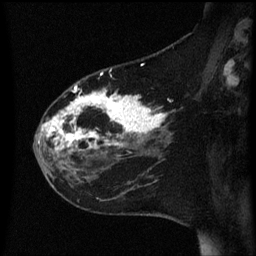
Breast MRI (dynamic contrast-enhanced), one sagittal slice. Position 20 of 60 along the scan axis. Dynamic contrast-enhanced series, image 2 of 3 at this slice position (ordered by acquisition). 1.5 T. TE 4.2 ms, TR 8.4 ms. 2.2 mm slice thickness. 256 × 256 image matrix, field of view 200 × 200 mm. Patient: female, 35 years. Case-level facts recorded for this patient, not image findings: setting: breast cancer imaged before/during neoadjuvant chemotherapy; receptor status: HER2-positive.
Structures marked on this image (semi-automatic segmentation, software-assisted and operator-edited):
- analysis volume of interest (the breast-tissue region the enhancement analysis was run in; not a lesion): box from (x=34, y=78) to (x=173, y=163) px
- tumour enhancement mask (voxels above the 70 % enhancement threshold inside the analysis volume of interest): (x=42, y=86)–(x=168, y=151)